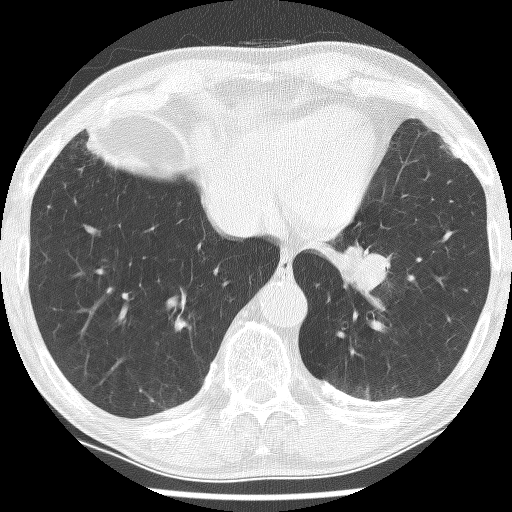
Axial slice from a low-dose chest CT screening exam; baseline screening round; lung window (W 1500 / L -600 HU); 2.5 mm slice thickness; 120 kVp; 512 × 512 image matrix, field of view 320 × 320 mm. Male, age 74 years at enrolment. Current smoker at enrolment.
- Expert-annotated lung lesion, bounding box (x1, y1, x2, y2) in pixels: (313, 218, 414, 310).
- Screening reader's record for this exam (one nodule recorded; not confirmed to be the boxed lesion): non-calcified nodule or mass ≥4 mm, left lower lobe, 30 × 27 mm, spiculated (stellate) margins, soft tissue attenuation.
- Lung cancer was diagnosed 151 days after this screen: adenocarcinoma, NOS, left lower lobe, stage IIIA (AJCC 6th edition), 49 mm at pathology.